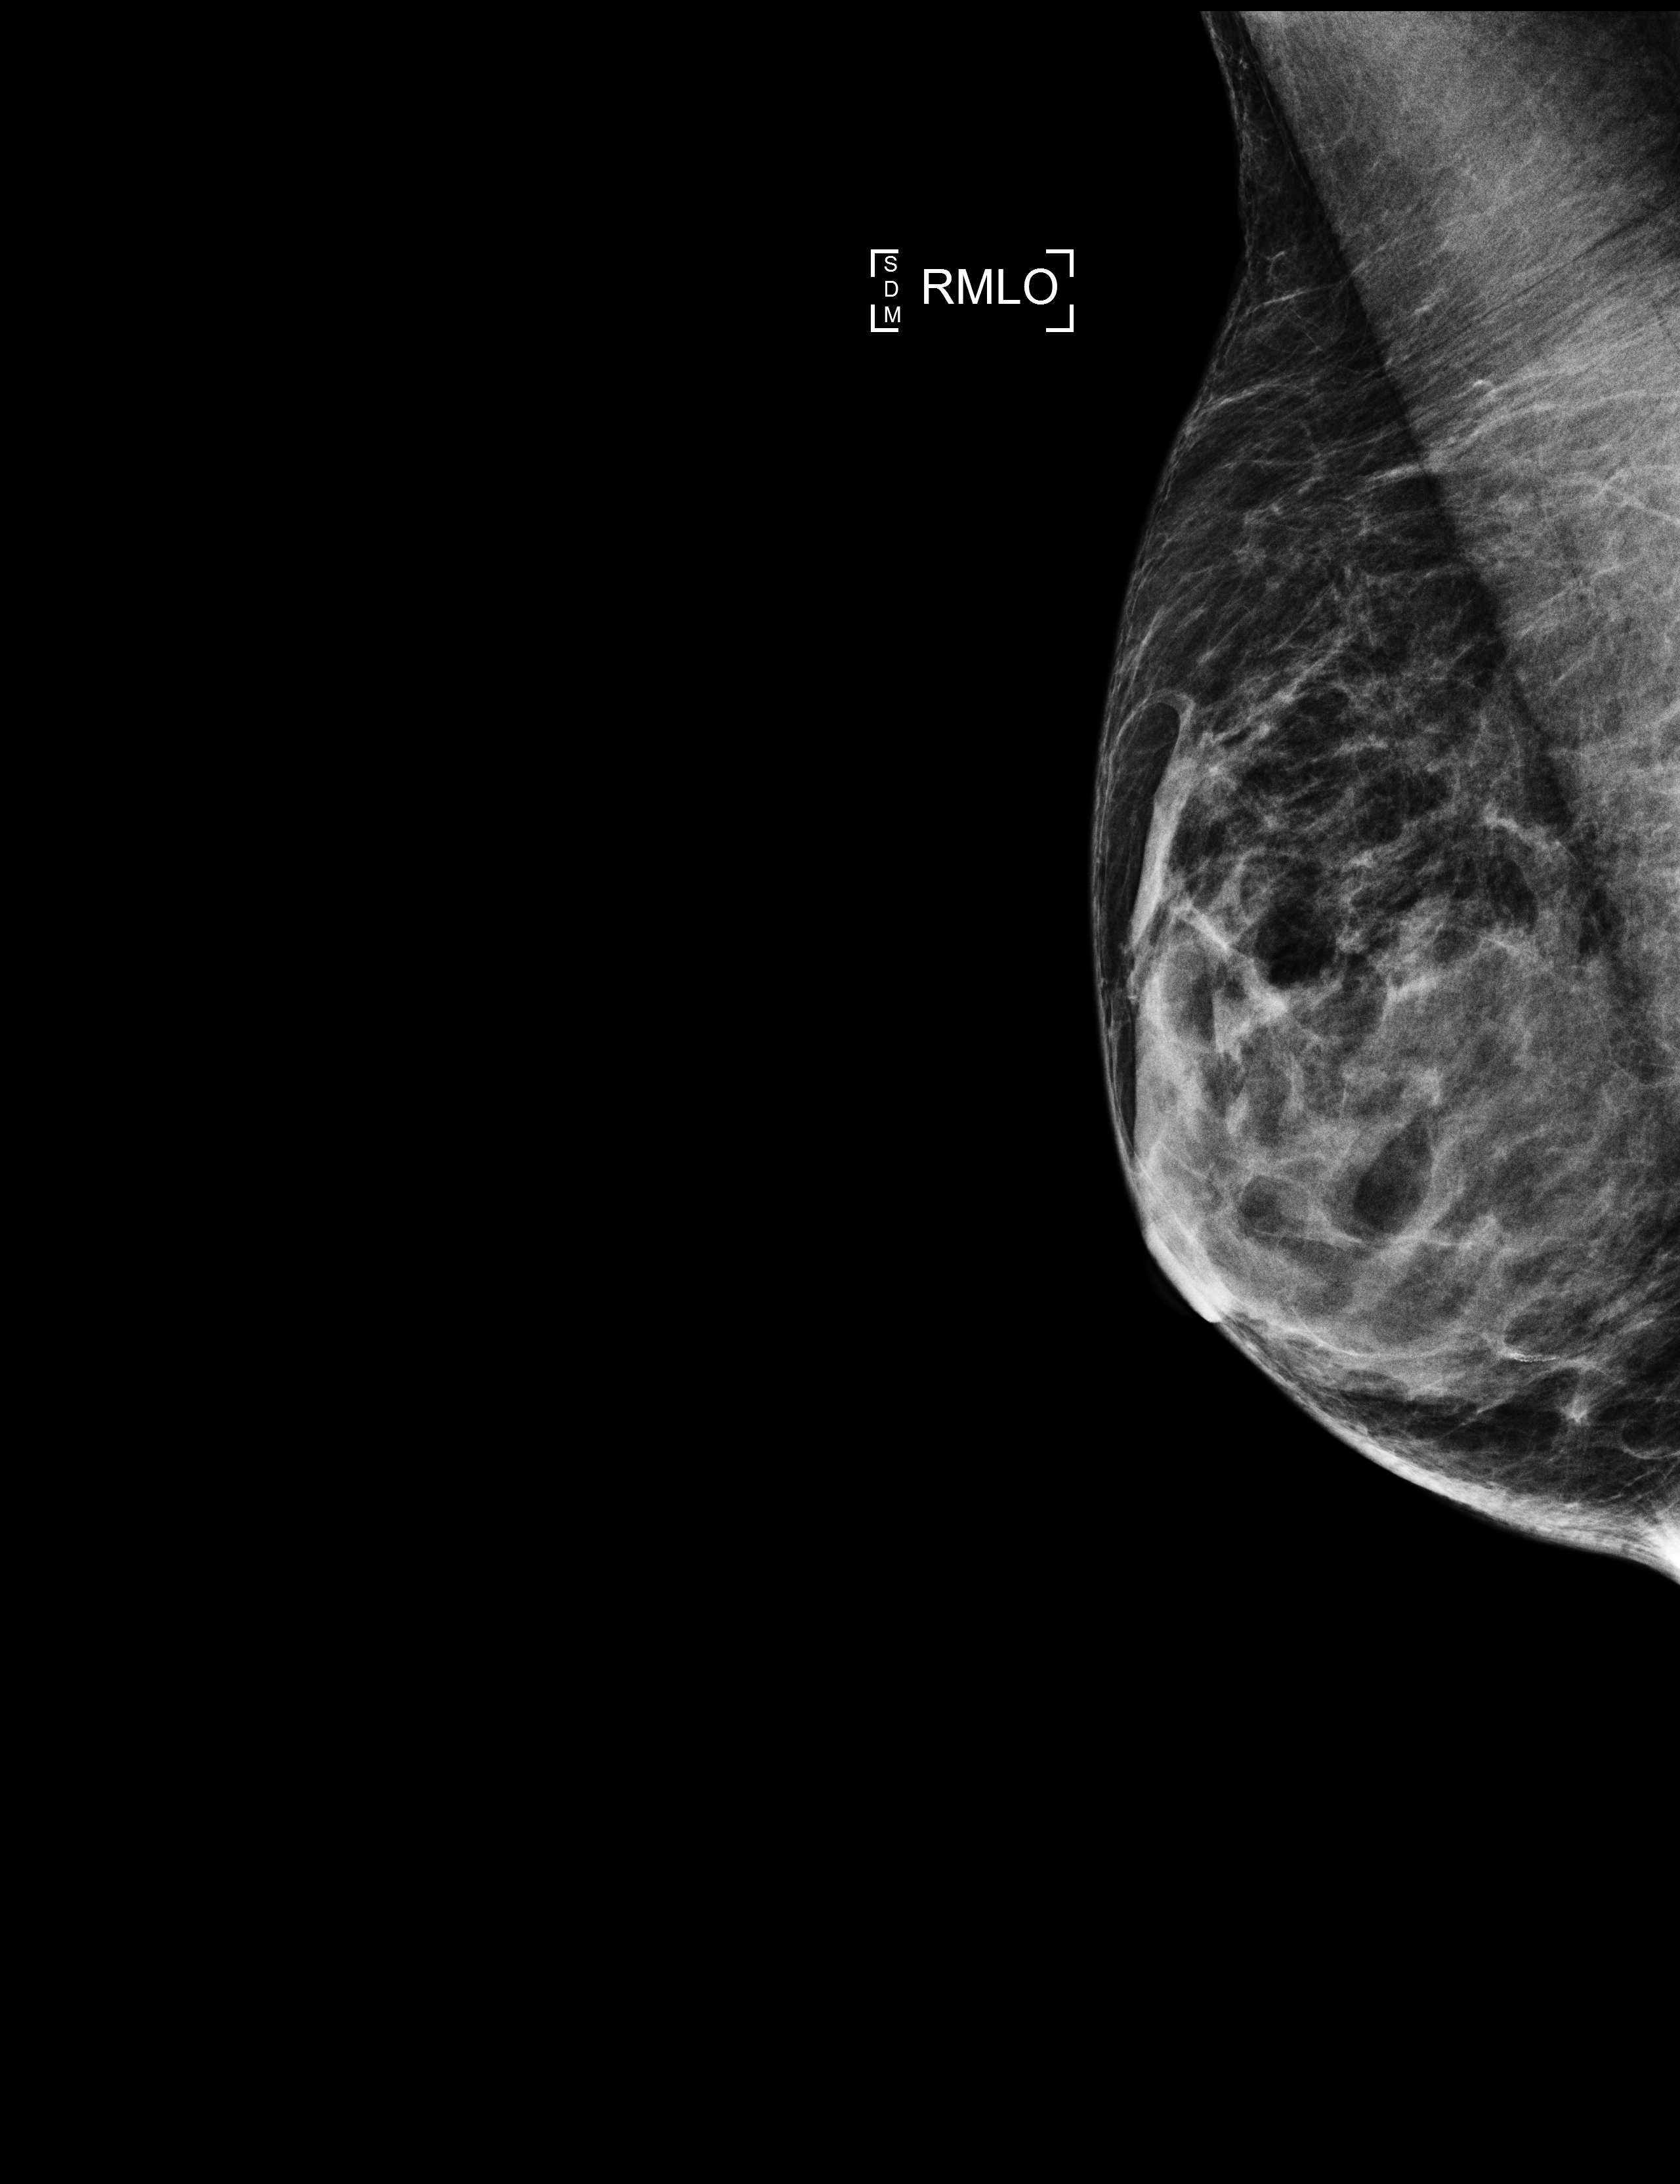
Full-field digital mammogram (FFDM); right breast; mediolateral oblique (MLO) view; annual screening mammography examination; compressed breast thickness 37 mm; system: Selenia Dimensions. Female patient, age 66 years.
Breast density at the screening exam (both breasts): heterogeneously dense (BI-RADS density category c). Final BI-RADS category for the screening round (tomosynthesis exam, both breasts): category 1. Recall: no recall after this screen.